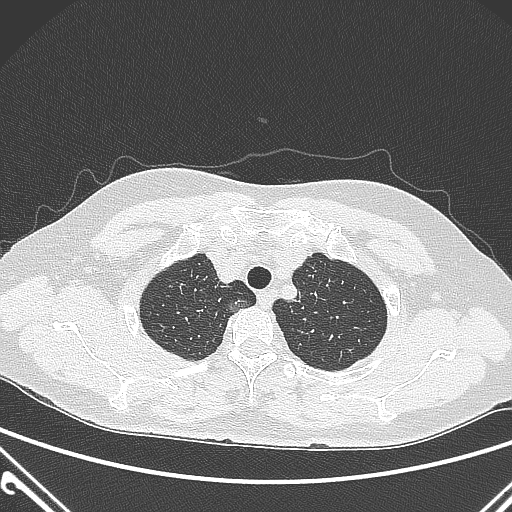
Chest CT, one axial slice. Position 244 of 300 along the scan axis. 120 kVp. Lung window (W 1500 / L -600 HU). 512 × 512 image matrix. Patient: female, 54 years. Case-level facts recorded for this patient, not image findings: clinical TNM (as recorded): T1a N0 M0; histopathological grade: G1.
Annotated regions visible in this slice (bounding box drawn by a radiologist):
- lung tumour (recorded histology: adenocarcinoma): bounding box <219,298,253,319> (left, top, right, bottom; pixels)